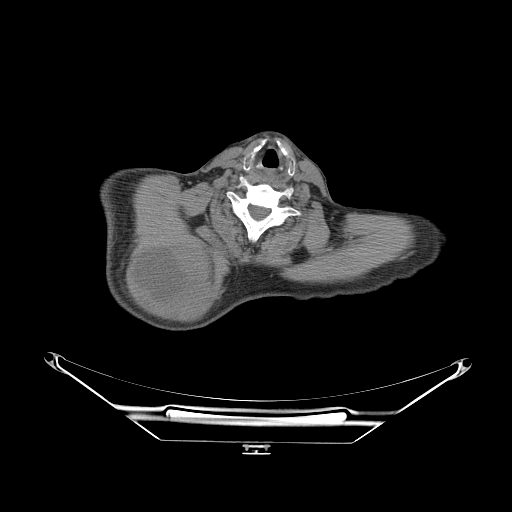
CT of an extremity soft-tissue mass (from a PET/CT study), one axial slice; soft-tissue window (W 400 / L 40 HU); 3.75 mm slice thickness; 512 × 512 image matrix. Male patient. Case-level facts recorded for this patient, not image findings: histological type: pleiomorphic spindle cell undifferentiated; grade: high; site of the primary tumour: right parascapusular.
Outlined on this slice (expert contour drawn on MRI and transferred to this co-registered scan by the dataset authors):
- gross tumour volume including surrounding oedema: bounding box (x1, y1, x2, y2) in pixels: (126, 242, 232, 316)
- gross tumour volume (mass): (132, 247, 206, 314)